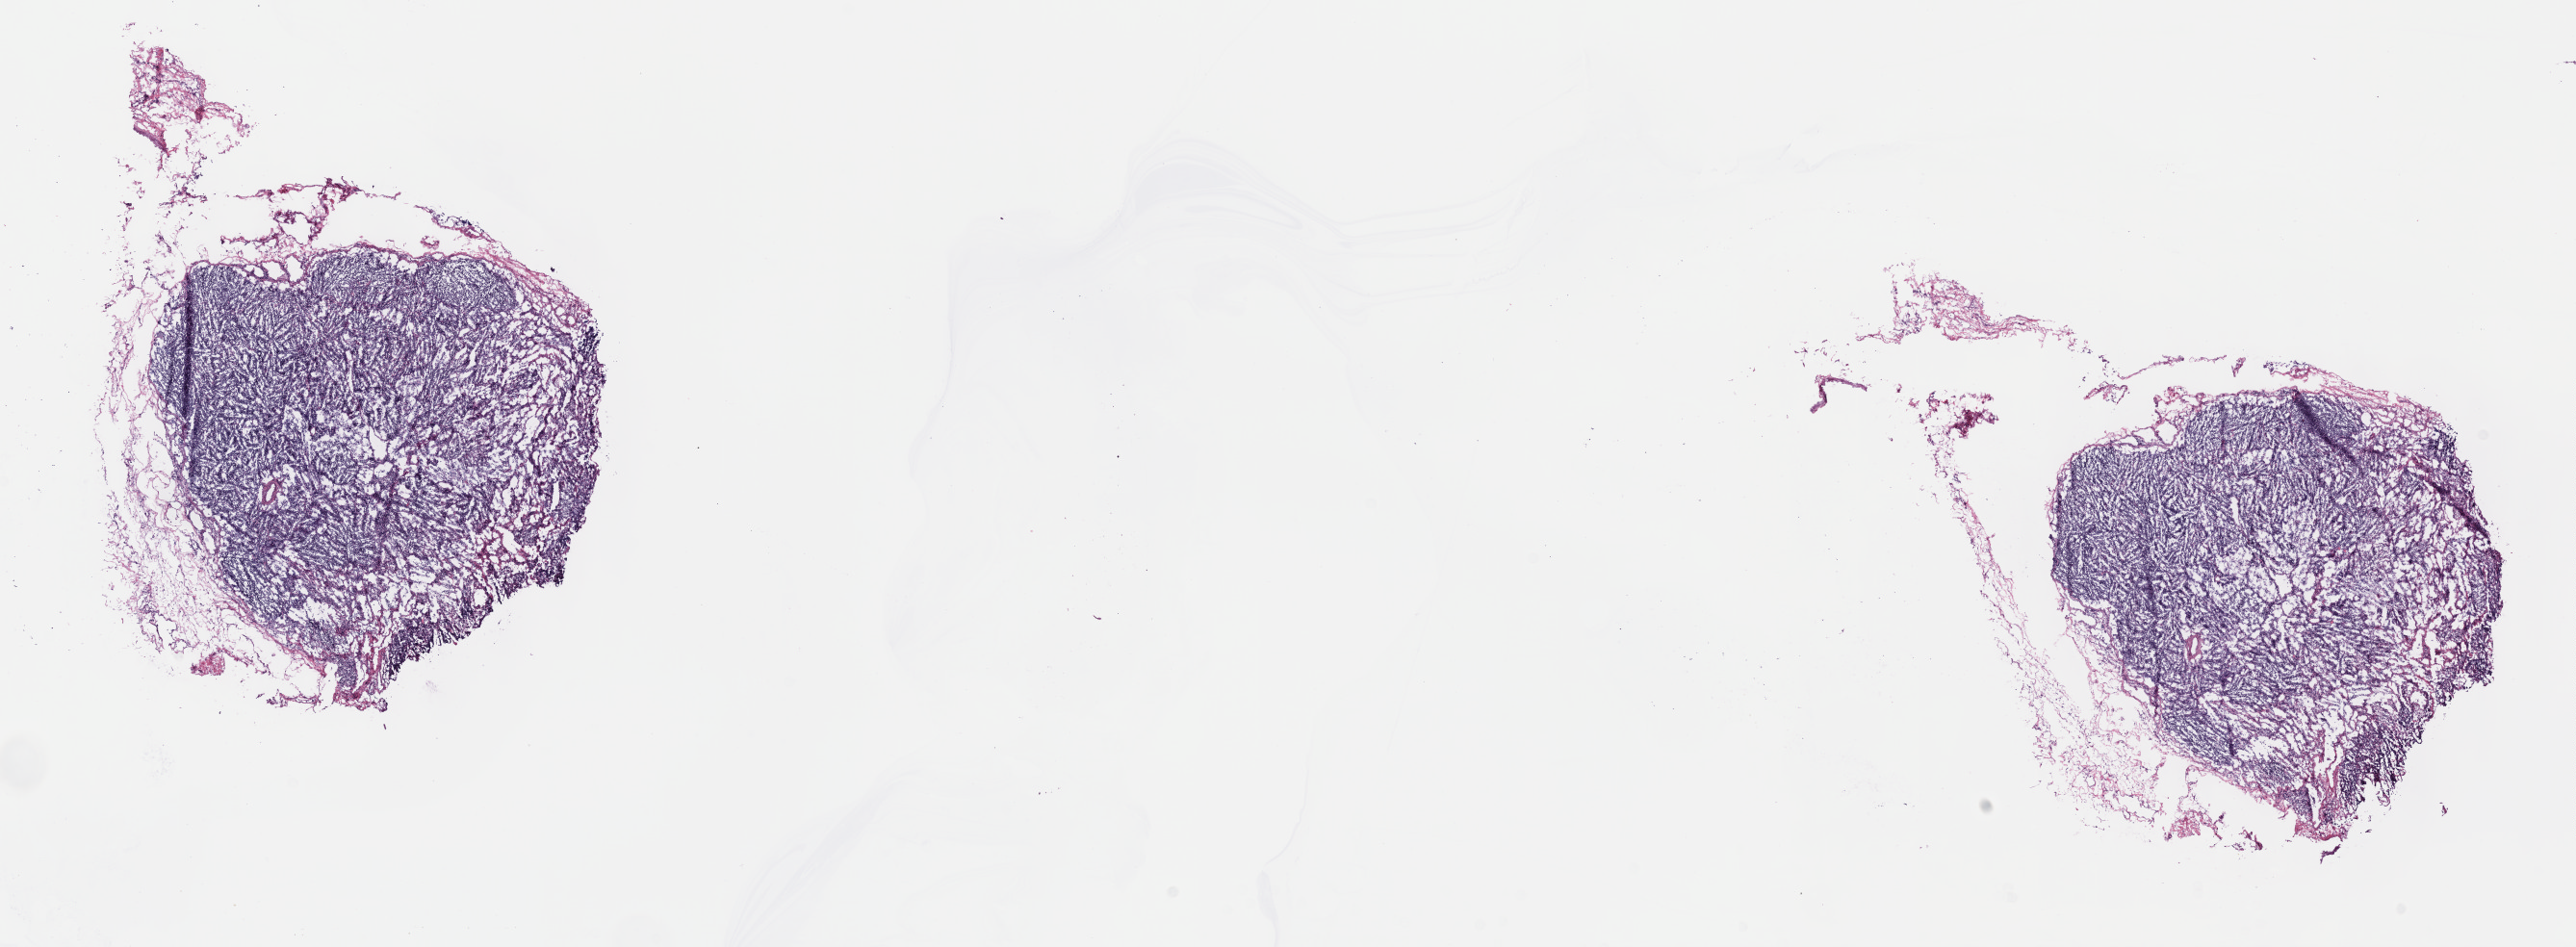
Digitized H&E tissue section (whole slide) — low-resolution overview of the scanned area, about 21.6 x 8.0 mm (slide scanned at 40x), frozen section, bile duct, primary tumour sample. Female patient; age at initial diagnosis 70 years. Histologic grade: G3 (poorly differentiated). Pathologist review of this section (percent, as recorded): tumour cells 70%, tumour nuclei 70%, normal cells 0%, stromal cells 30%, necrosis 0%. Infiltration values recorded for this section: lymphocyte infiltration 5%, monocyte infiltration 1%, neutrophil infiltration 3%.
TNM: T3 N0 M0. Diagnosis: Cholangiocarcinoma (intrahepatic bile duct). AJCC pathologic stage: III (7th edition).